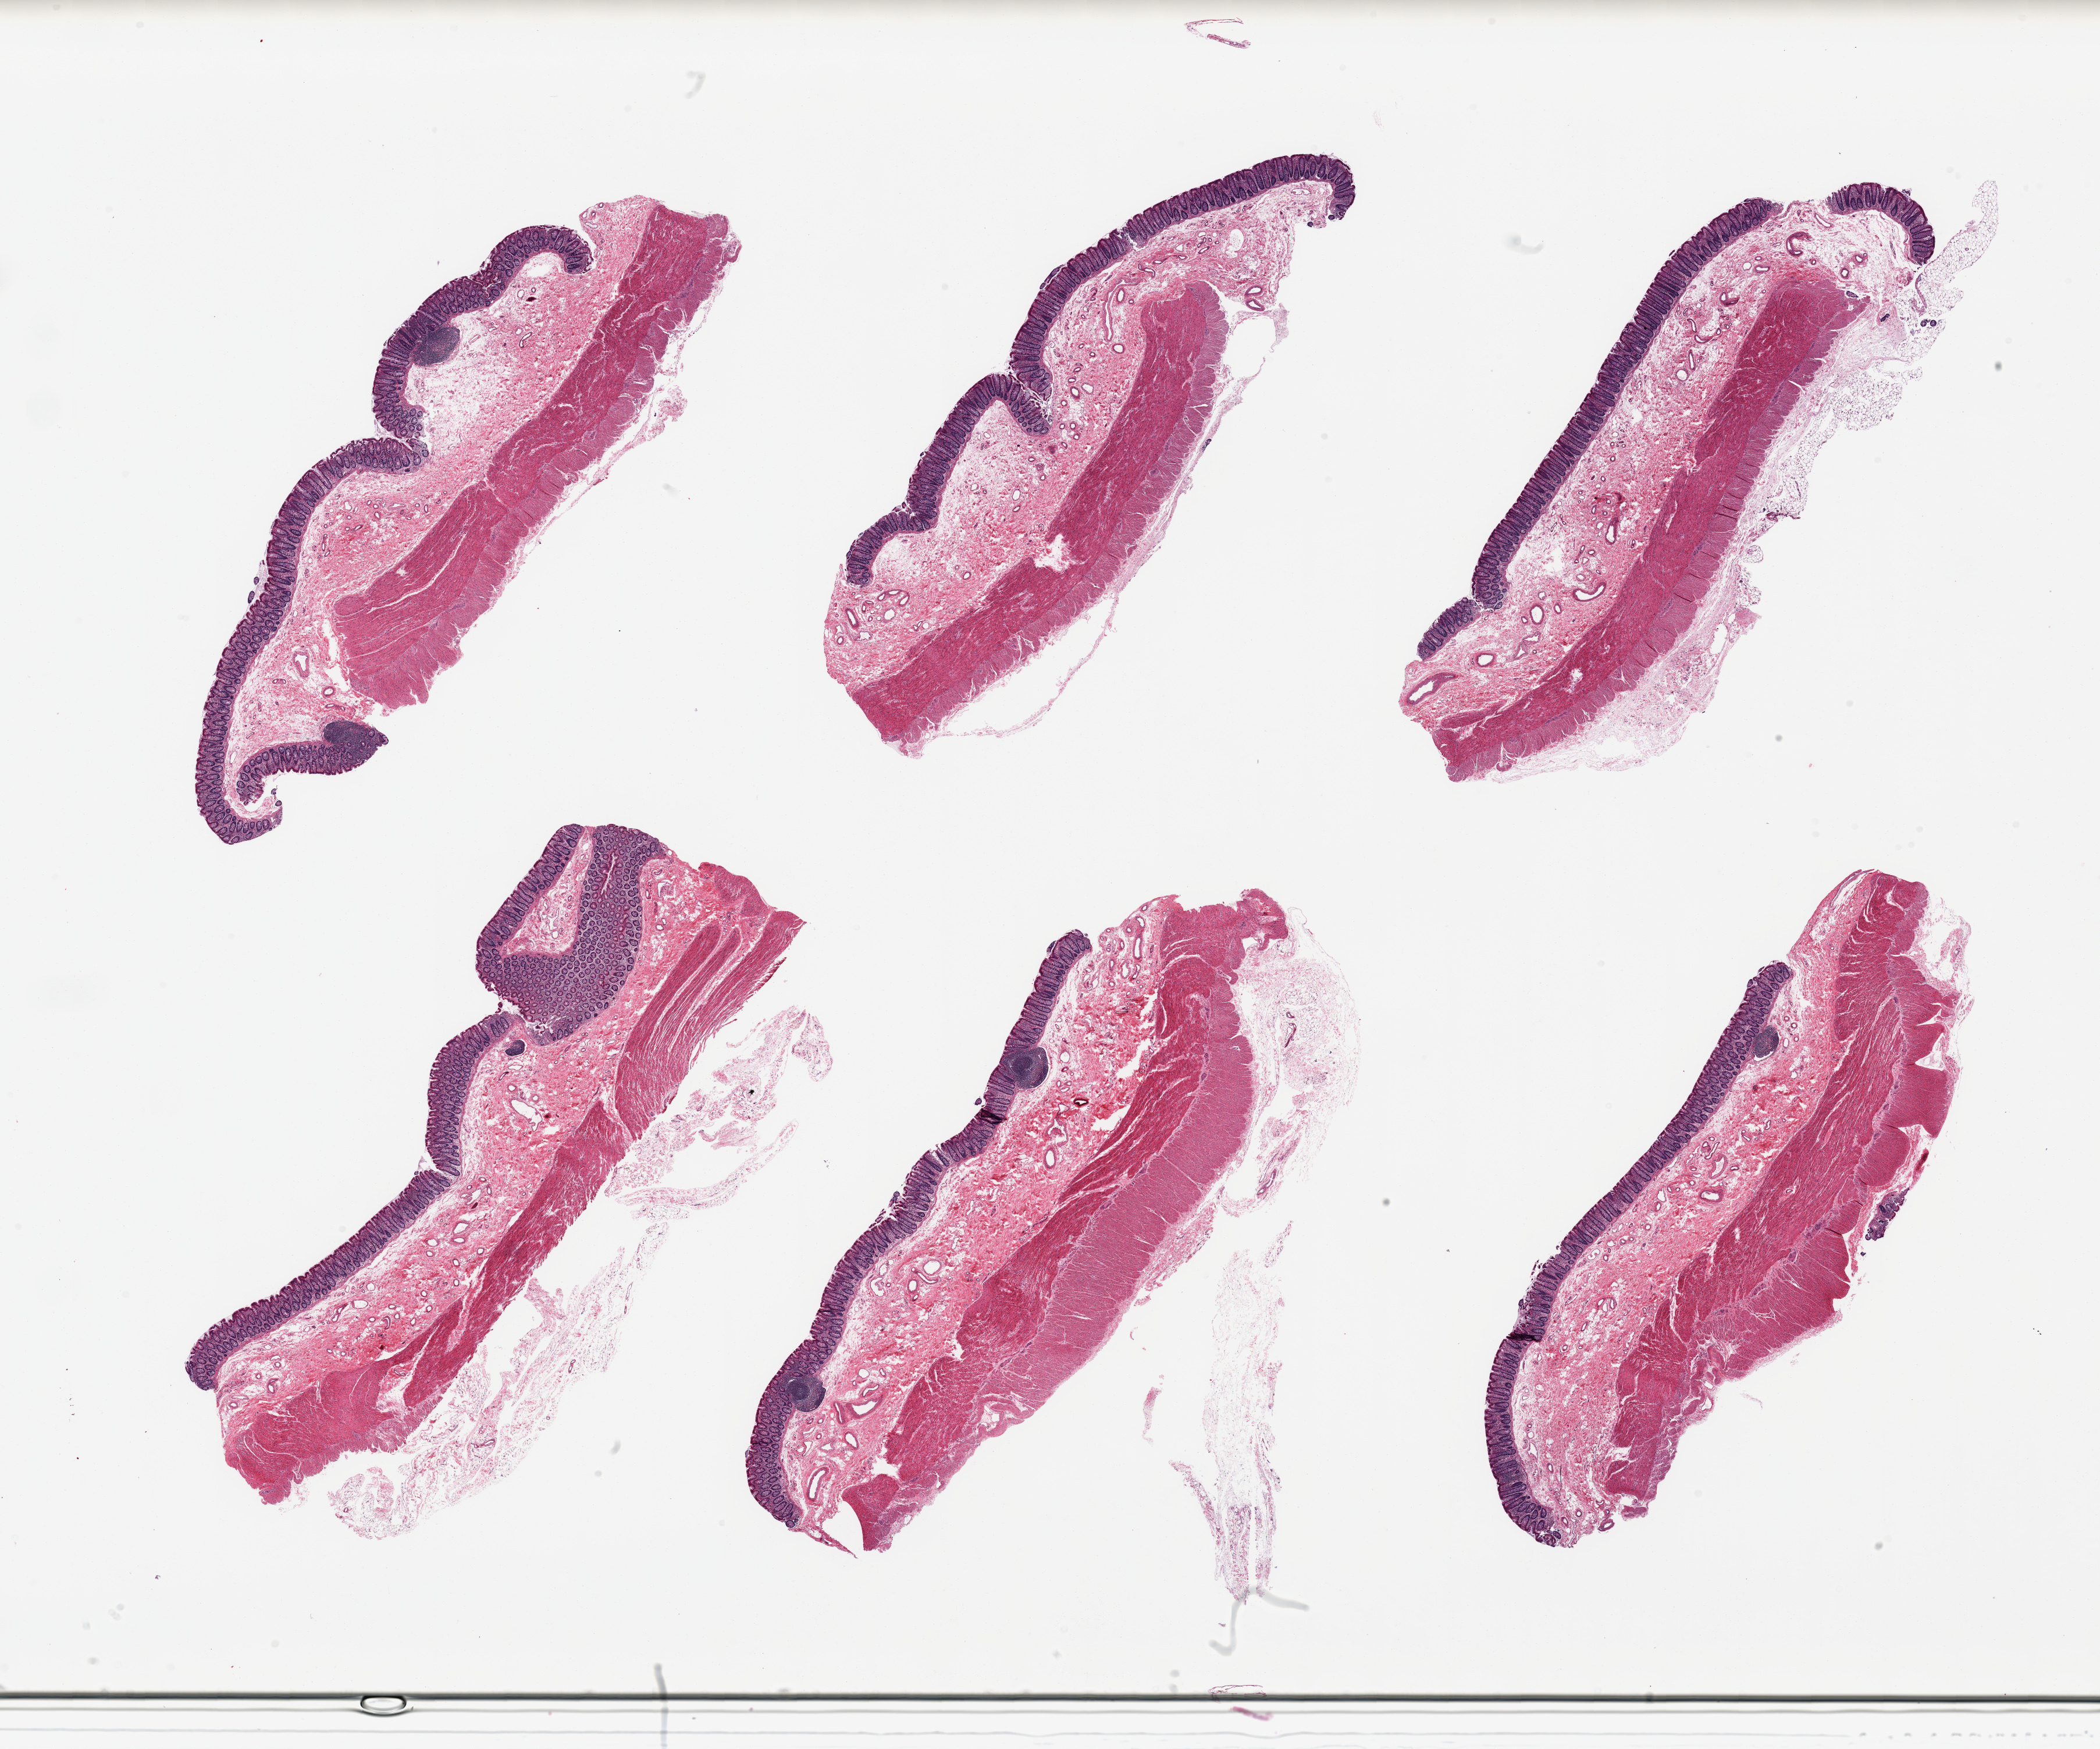
Whole-slide image, hematoxylin and eosin (H&E) stain — low-resolution overview of the scanned area, about 28.5 x 23.8 mm, PAXgene-fixed paraffin-embedded (PFPE) section, target tissue: transverse colon, donor tissue sample. Male donor.
Review note (as recorded): 6 pieces, well-preserved mucosa up to ~0.35mm, ~10-15% thickness.